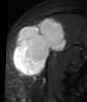
MRI of an extremity soft-tissue mass, one axial slice; position 26 of 48 along the scan axis; STIR; MR volume resampled by the dataset authors to the PET/CT grid (not the native acquisition matrix); 87 × 102 image matrix, field of view 85 × 100 mm. Female patient. From the clinical record (not read from this slice): histological type: synovial sarcoma; grade: intermediate; site of the primary tumour: right thigh.
Outlined on this slice (expert contour drawn on MRI and transferred to this co-registered scan by the dataset authors):
- gross tumour volume including surrounding oedema: bounding box <13,18,66,76> (left, top, right, bottom; pixels)
- gross tumour volume (mass): <13,18,68,76>